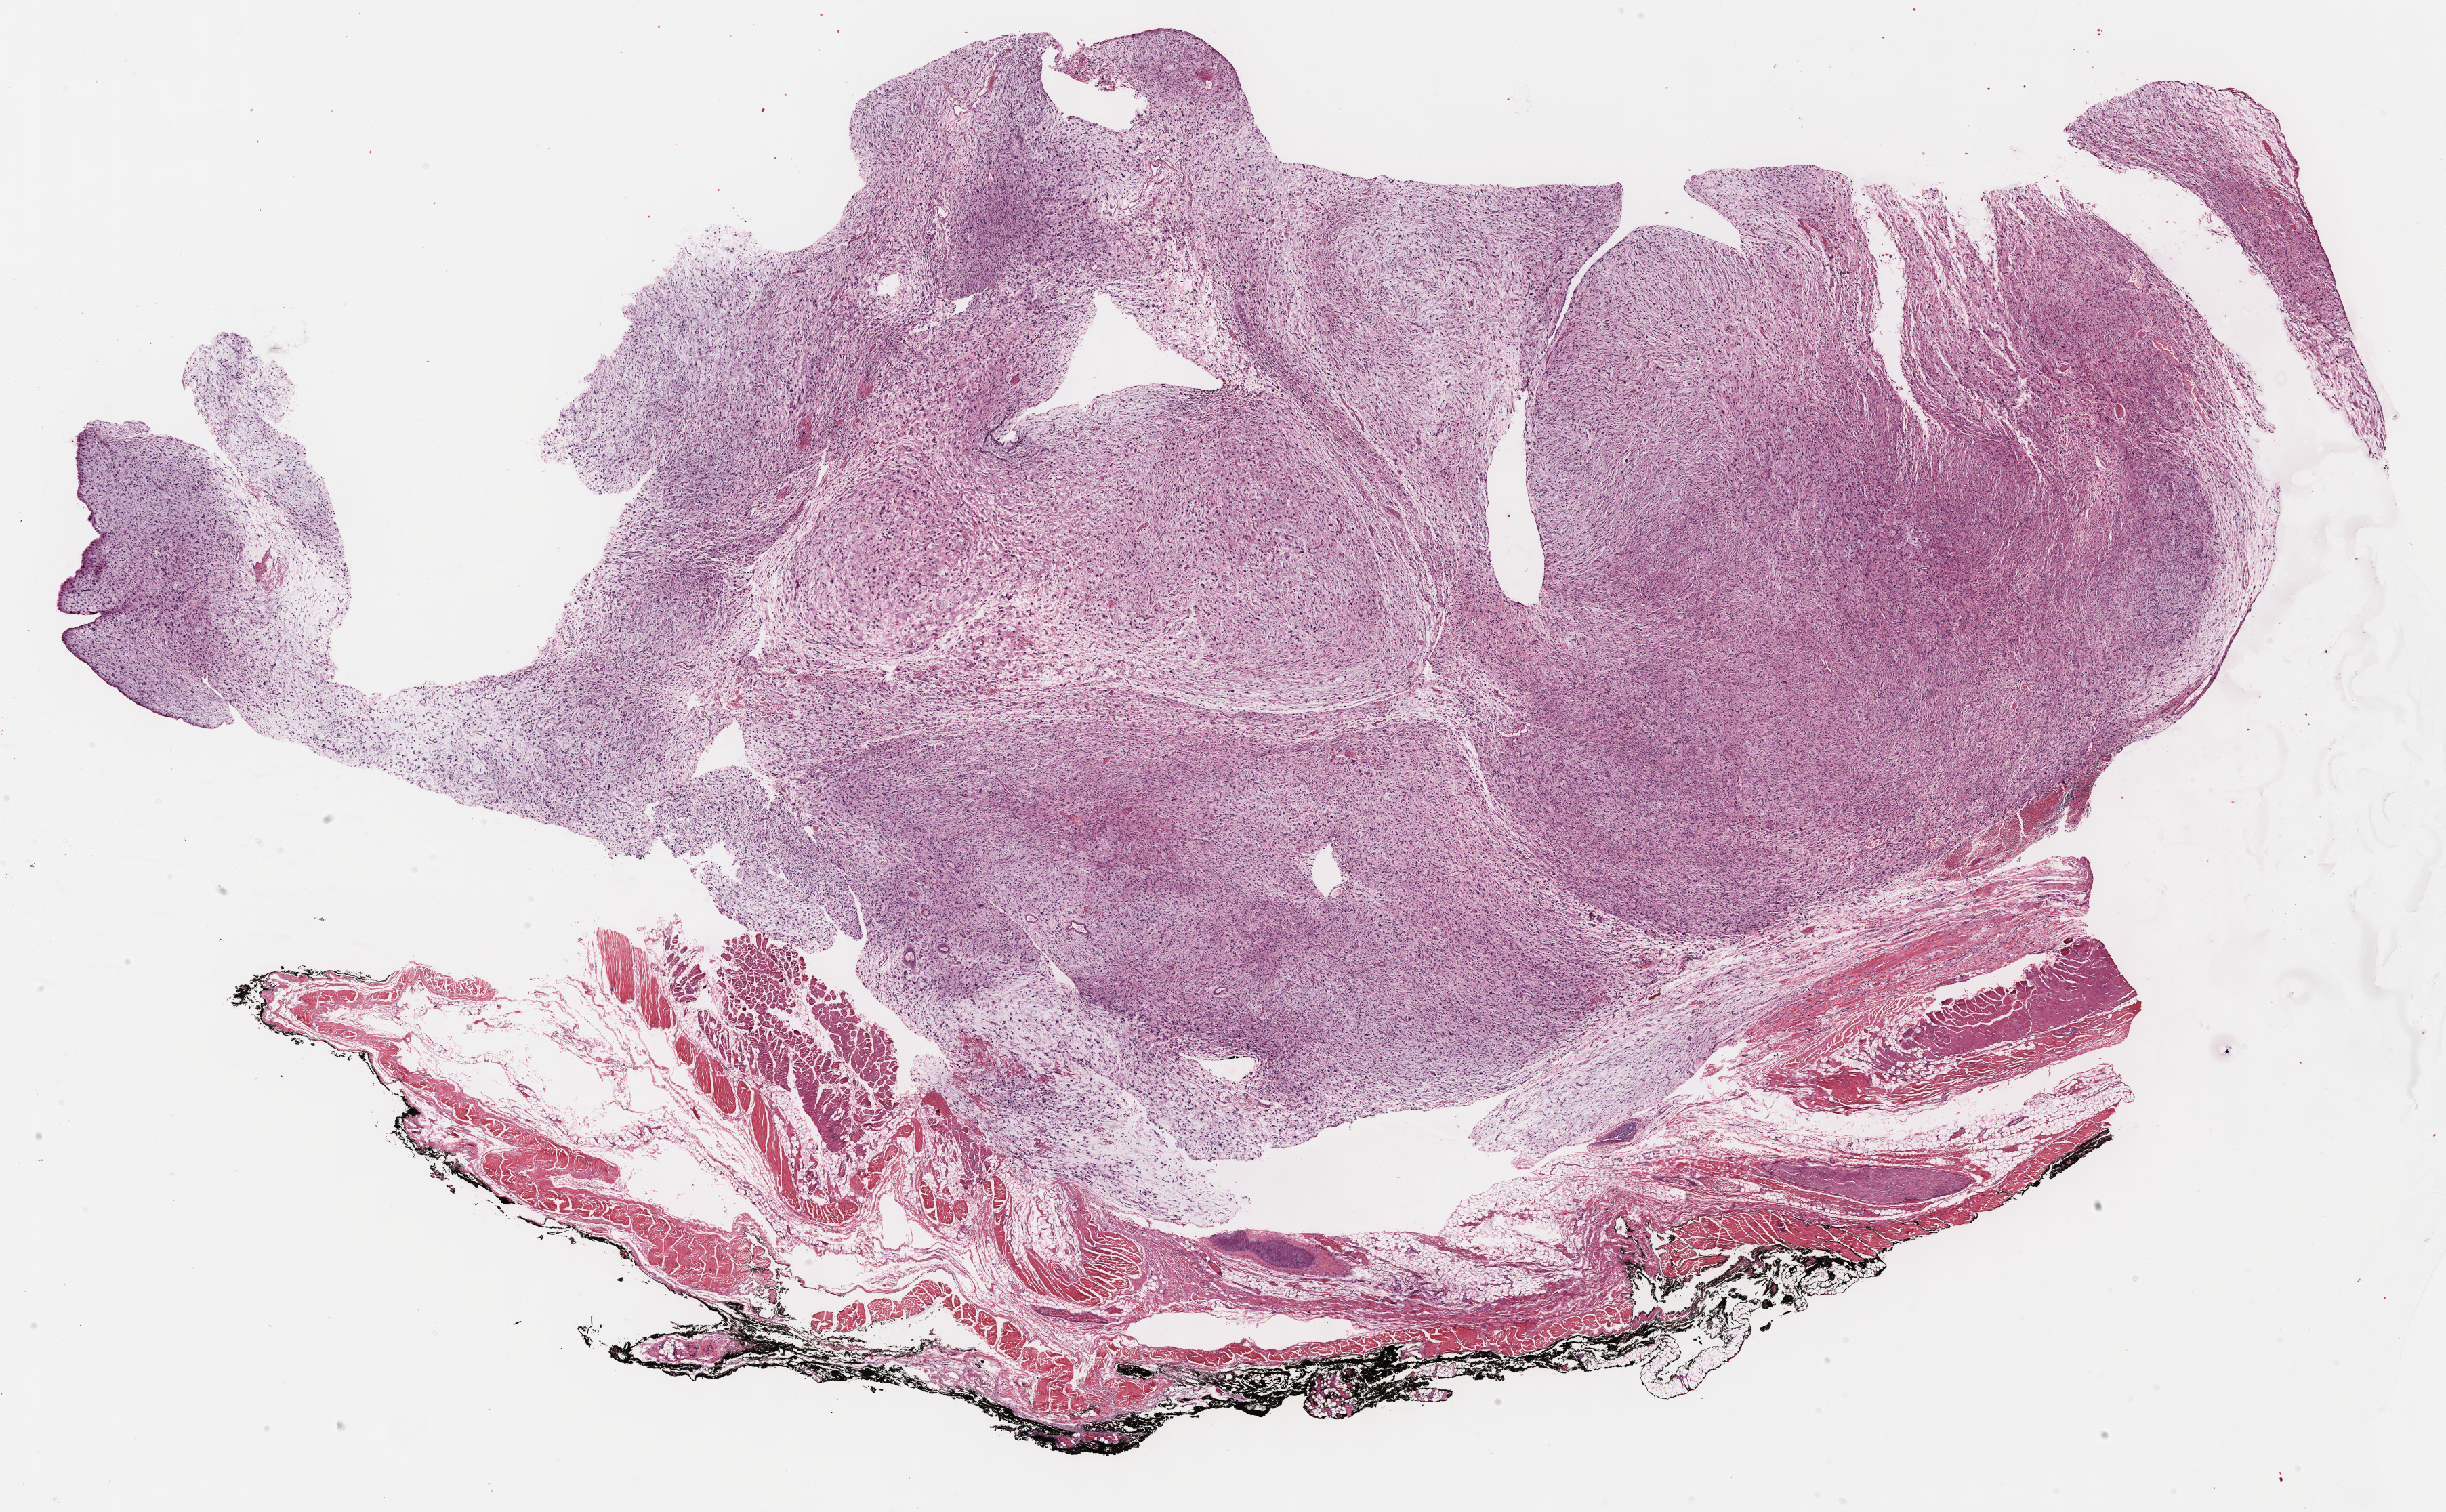
Digitized H&E-stained tissue section (whole slide), shown as a low-resolution overview of the whole scanned area (about 29.2 x 18.1 mm, from a 40x scan); FFPE section; sample: primary tumour, connective, subcutaneous and other soft tissues. Patient sex: male.
Diagnosis: Fibromyxosarcoma (connective, subcutaneous and other soft tissues of trunk, NOS).